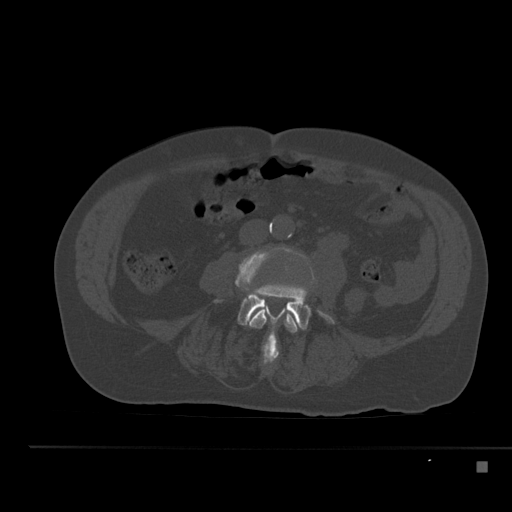
CT including the spine, one axial slice; slice 150 of 517 in the series (ordered by position); bone window (W 1800 / L 400 HU); 512 × 512 image matrix, field of view 408 × 408 mm. Patient: male, 70 years. From the clinical record (not read from this slice): primary cancer: renal; vertebrae with lytic lesions (as recorded): T4, T6, T10, T12, L3, L4, L5.
Annotated regions visible in this slice (semi-automatically segmented with operator editing):
- L3 vertebra: bounding box [x1, y1, x2, y2] px = [236, 248, 298, 365]
- L4 vertebra: [237, 282, 334, 365]